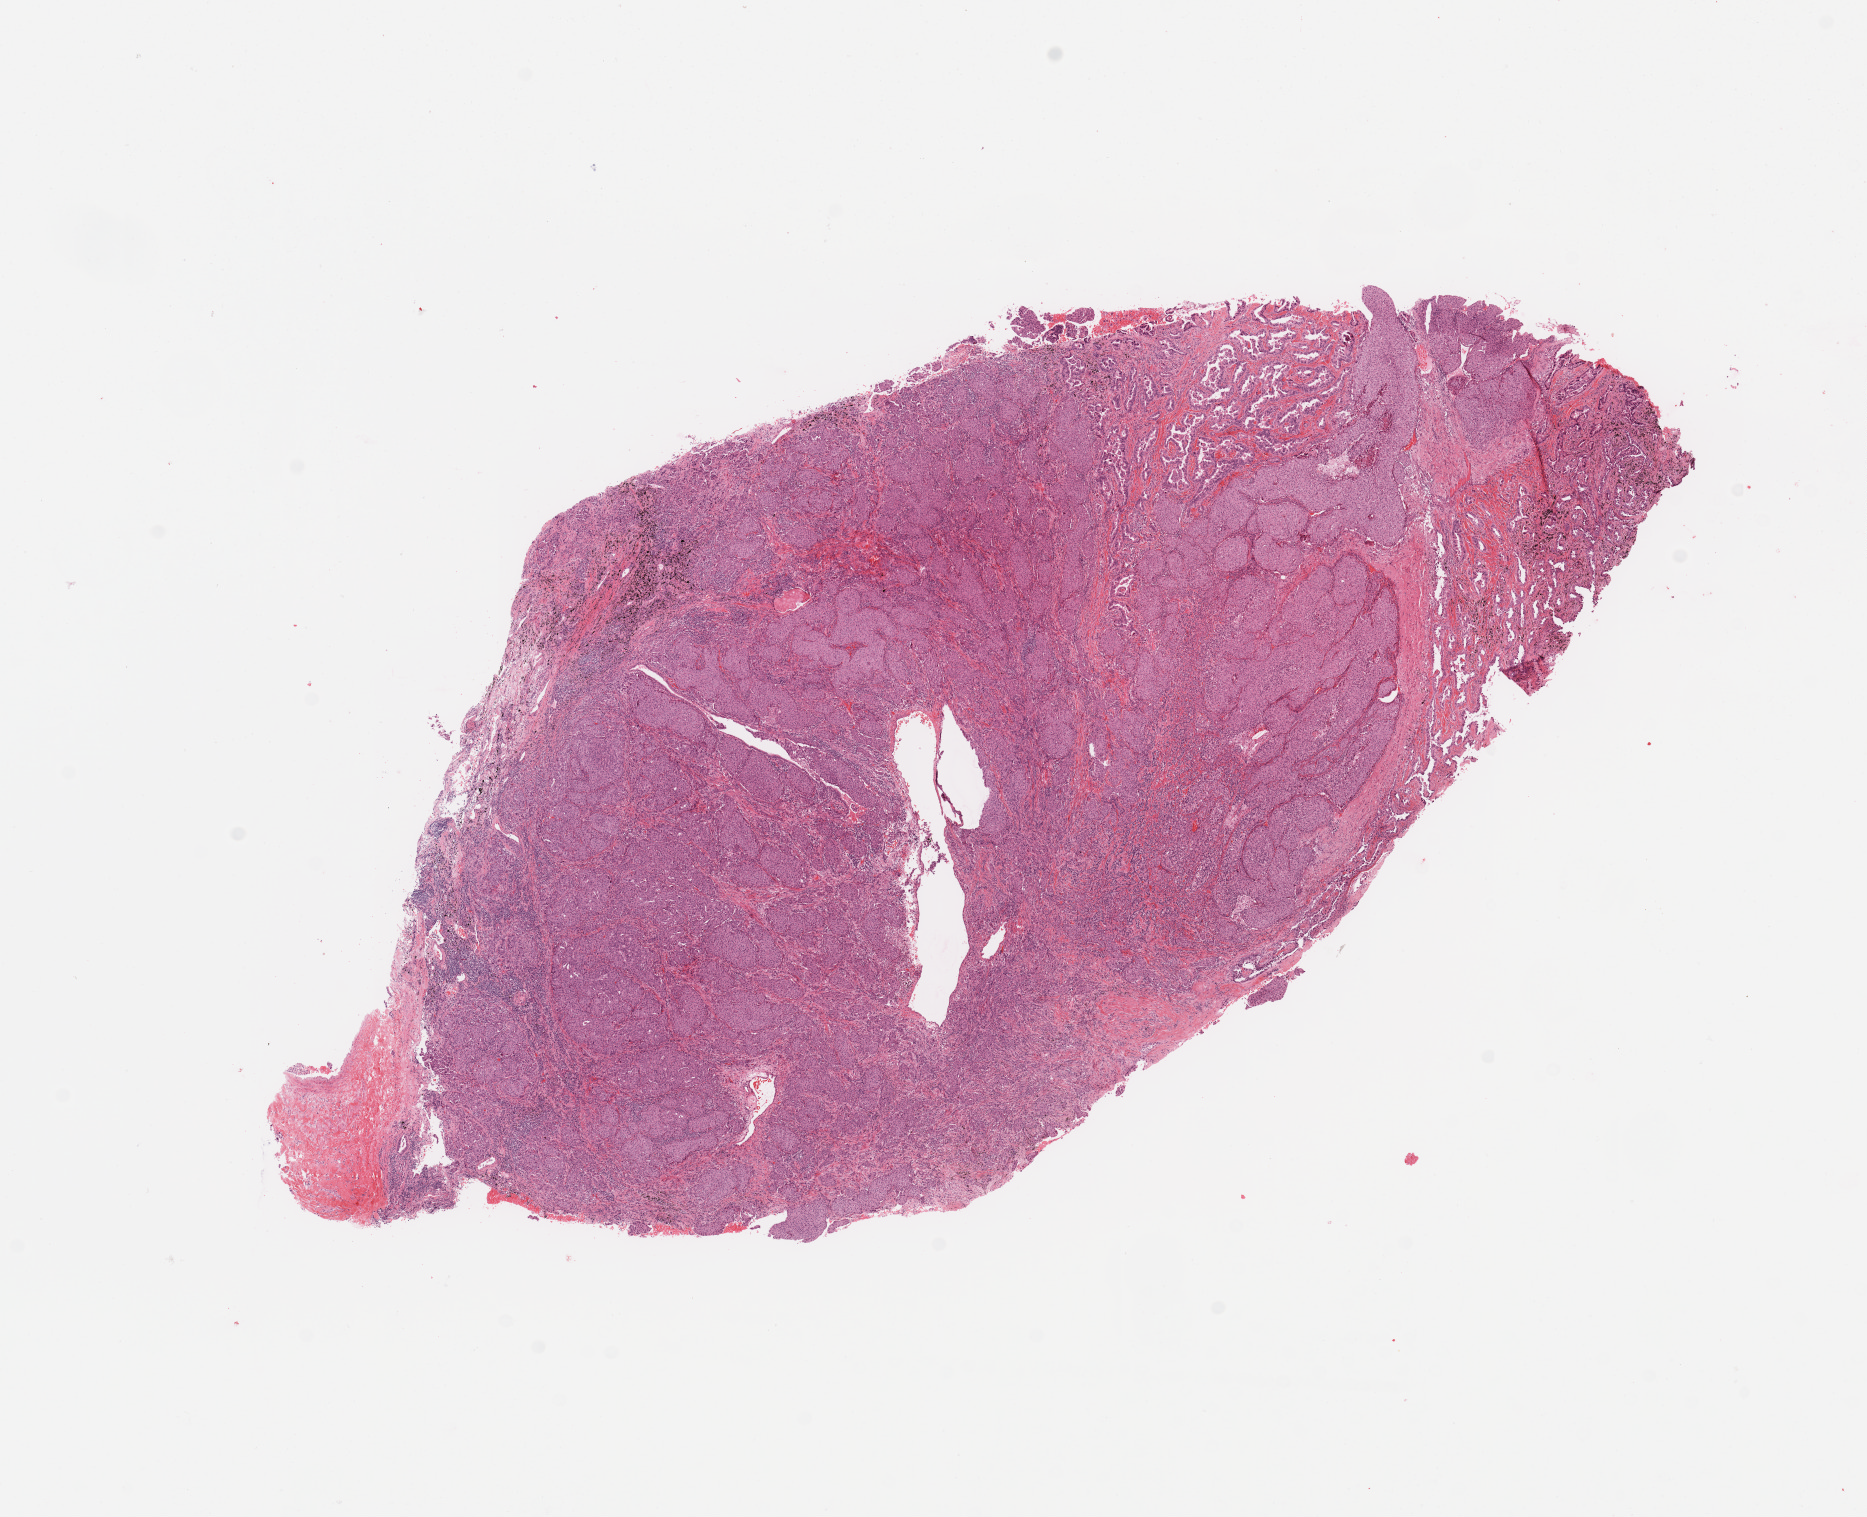
Digitized H&E-stained tissue section (whole slide) — low-resolution overview of the scanned area, about 14.8 x 12.0 mm (slide scanned at 20x), tumour tissue sample, sampled site: lung. Male, 77 y/o. Histologic grade: G3 (poorly differentiated). Pathologist review of this section (percent, as recorded): tumour nuclei 90%, necrosis 2%.
Primary tumour site (as recorded): left upper lobe. Histologic diagnosis: Adenocarcinoma, NOS. AJCC pathologic stage: IIB.